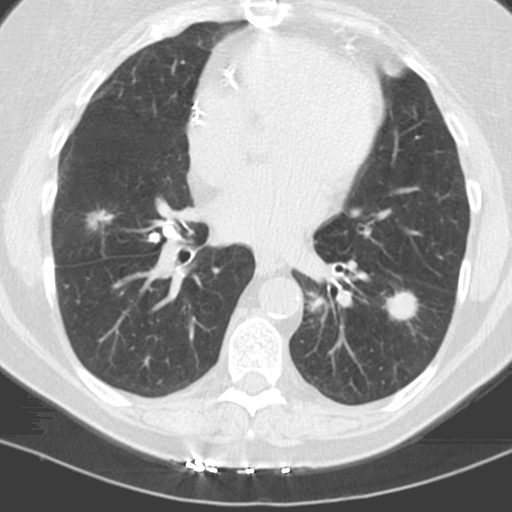
Chest CT (low-dose screening protocol), one axial image. Baseline annual screen. Lung window (W 1500 / L -600 HU). Standard (soft-tissue) reconstruction kernel (C). Slice 72 of 121 in the series. 512 × 512 image matrix. Female, age 60 years at enrolment. Former smoker at enrolment.
2 expert-annotated lung lesions on this slice (largest first), bounding box [x1, y1, x2, y2] px = [287, 279, 338, 332]; [376, 286, 425, 328]. The screening reader recorded 3 non-calcified nodules or masses ≥4 mm on this exam (left lower lobe, left lower lobe, right middle lobe); which of them these boxes mark is not recorded. Official screen result: positive, change unspecified: nodule(s) >= 4 mm or enlarging nodule(s), mass(es), or other non-specific abnormalities suspicious for lung cancer. Later outcome: lung cancer diagnosed 96 days after this screen — adenocarcinoma, NOS, left lower lobe, stage IV (AJCC 6th edition), 22 mm at pathology.